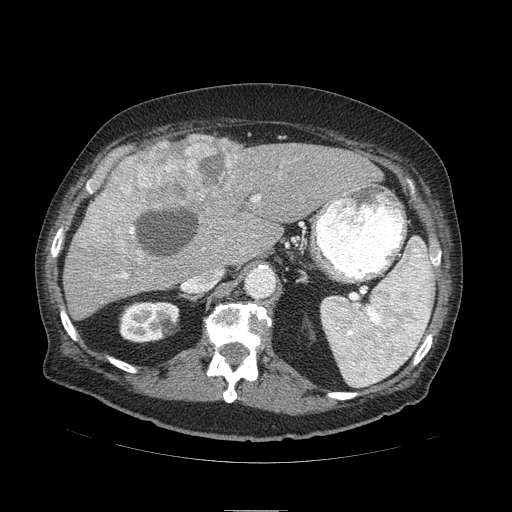
Contrast-enhanced abdominal CT (liver protocol), one axial slice; slice 59 of 103 in the series (ordered by position); 120 kVp; soft-tissue window (W 400 / L 40 HU); 2.5 mm slice thickness; 512 × 512 image matrix, field of view 440 × 440 mm. From the clinical record (not read from this slice): diagnosis: hepatocellular carcinoma (patient treated with transarterial chemoembolisation; whether this scan precedes or follows treatment is not stated here); TNM stage (as recorded): Stage-IIIA; Child-Pugh class: B; tumour nodularity: multinodular; tumour size: 13 cm.
Outlined on this slice (semi-automatically segmented with operator editing):
- liver parenchyma outside the tumour (the mass and vessels are separate outlines, so this box may not span the whole liver): box from (x=62, y=134) to (x=382, y=320) px
- mass: (x=76, y=134)–(x=245, y=251)
- liver vessels: (x=121, y=196)–(x=260, y=278)